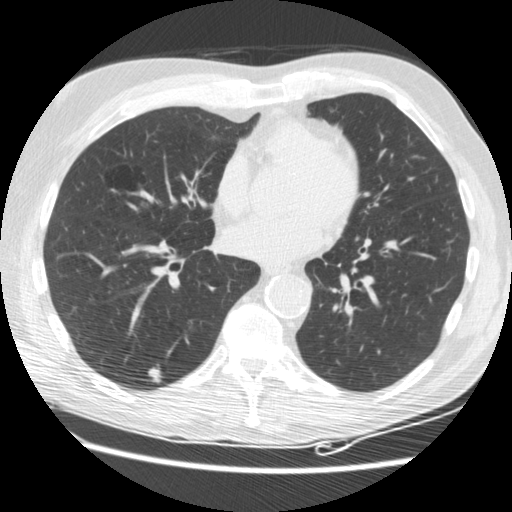
Low-dose screening chest CT, one axial slice; position 77 of 176 along the scan axis; reconstruction kernel STANDARD; 120 kVp; lung window (W 1500 / L -600 HU); 2.5 mm slice thickness; 512 × 512 image matrix.
Annotated regions visible in this slice (expert manual segmentation):
- lesion 2 (tumor, lower lobe of right lung): bounding box <149,369,160,382> (left, top, right, bottom; pixels)